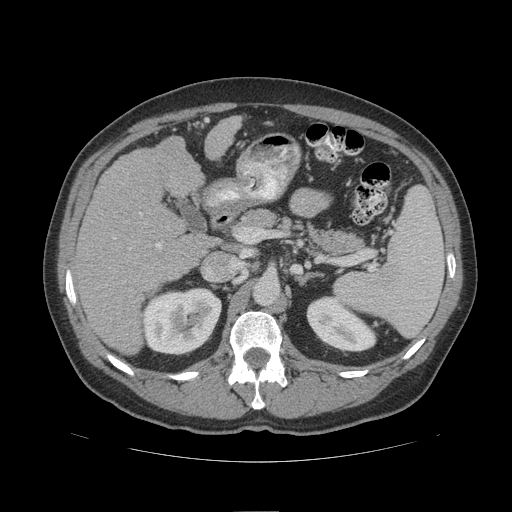
Contrast-enhanced abdominal CT (liver protocol), one axial slice; position 58 of 109 along the scan axis; reconstruction kernel STANDARD; 140 kVp; soft-tissue window (W 400 / L 40 HU); 512 × 512 image matrix, field of view 420 × 420 mm. Case-level facts recorded for this patient, not image findings: diagnosis: hepatocellular carcinoma (patient treated with transarterial chemoembolisation; whether this scan precedes or follows treatment is not stated here); TNM stage (as recorded): Stage-IIIB; Child-Pugh class: A; tumour nodularity: multinodular.
Annotated regions visible in this slice (semi-automatic segmentation, software-assisted and operator-edited):
- liver parenchyma outside the tumour (the mass and vessels are separate outlines, so this box may not span the whole liver): box from (x=76, y=116) to (x=242, y=354) px
- liver vessels: (x=140, y=213)–(x=161, y=248)